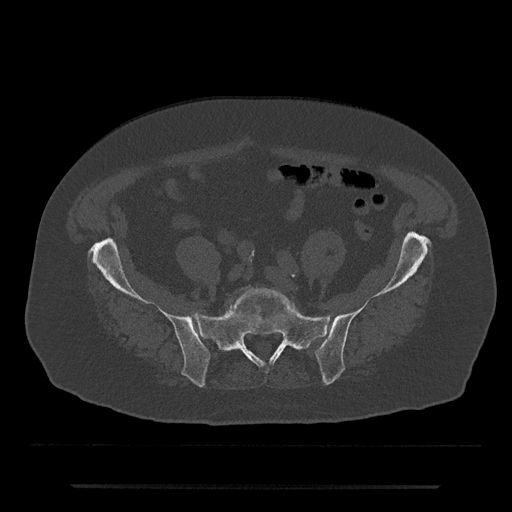
CT including the spine, one axial slice. Position 244 of 797 along the scan axis. Reconstruction kernel Br40s/3. 120 kVp. Bone window (W 1800 / L 400 HU). 512 × 512 image matrix. Male patient, age 80 years. Case-level facts recorded for this patient, not image findings: primary cancer: prostate.
Structures marked on this image (semi-automatic segmentation, software-assisted and operator-edited):
- L5 vertebra: bounding box (x1, y1, x2, y2) in pixels: (229, 287, 299, 315)